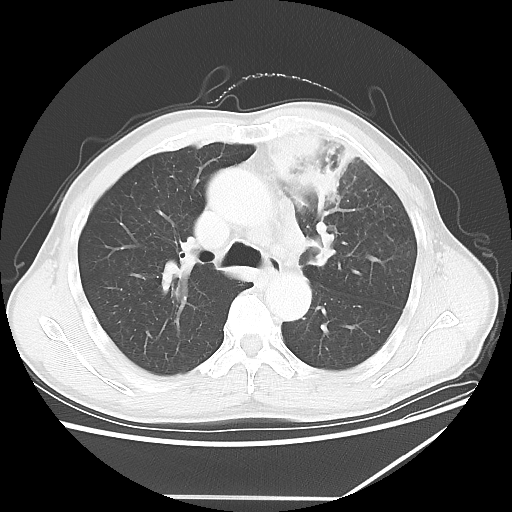
Chest CT, one axial slice. Slice 42 of 64 in the series (ordered by position). Reconstruction kernel LUNG. 100 kVp. Lung window (W 1500 / L -600 HU). 5 mm slice thickness. 512 × 512 image matrix, field of view 383 × 383 mm. Male patient, age 64 years. Case-level facts recorded for this patient, not image findings: clinical TNM (as recorded): T1c N1 M1; histopathological grade: G2.
Outlined on this slice (bounding box drawn by a radiologist):
- lung tumour (recorded histology: squamous cell carcinoma): bounding box (x1, y1, x2, y2) in pixels: (249, 114, 363, 226)